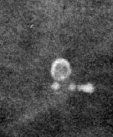
Region of interest cut from a scanned film mammogram (one marked finding); right breast; CC view.
Finding: calcifications, morphology skin, distribution regional; BI-RADS assessment category 2; benign; no additional work-up was recommended (benign without callback).